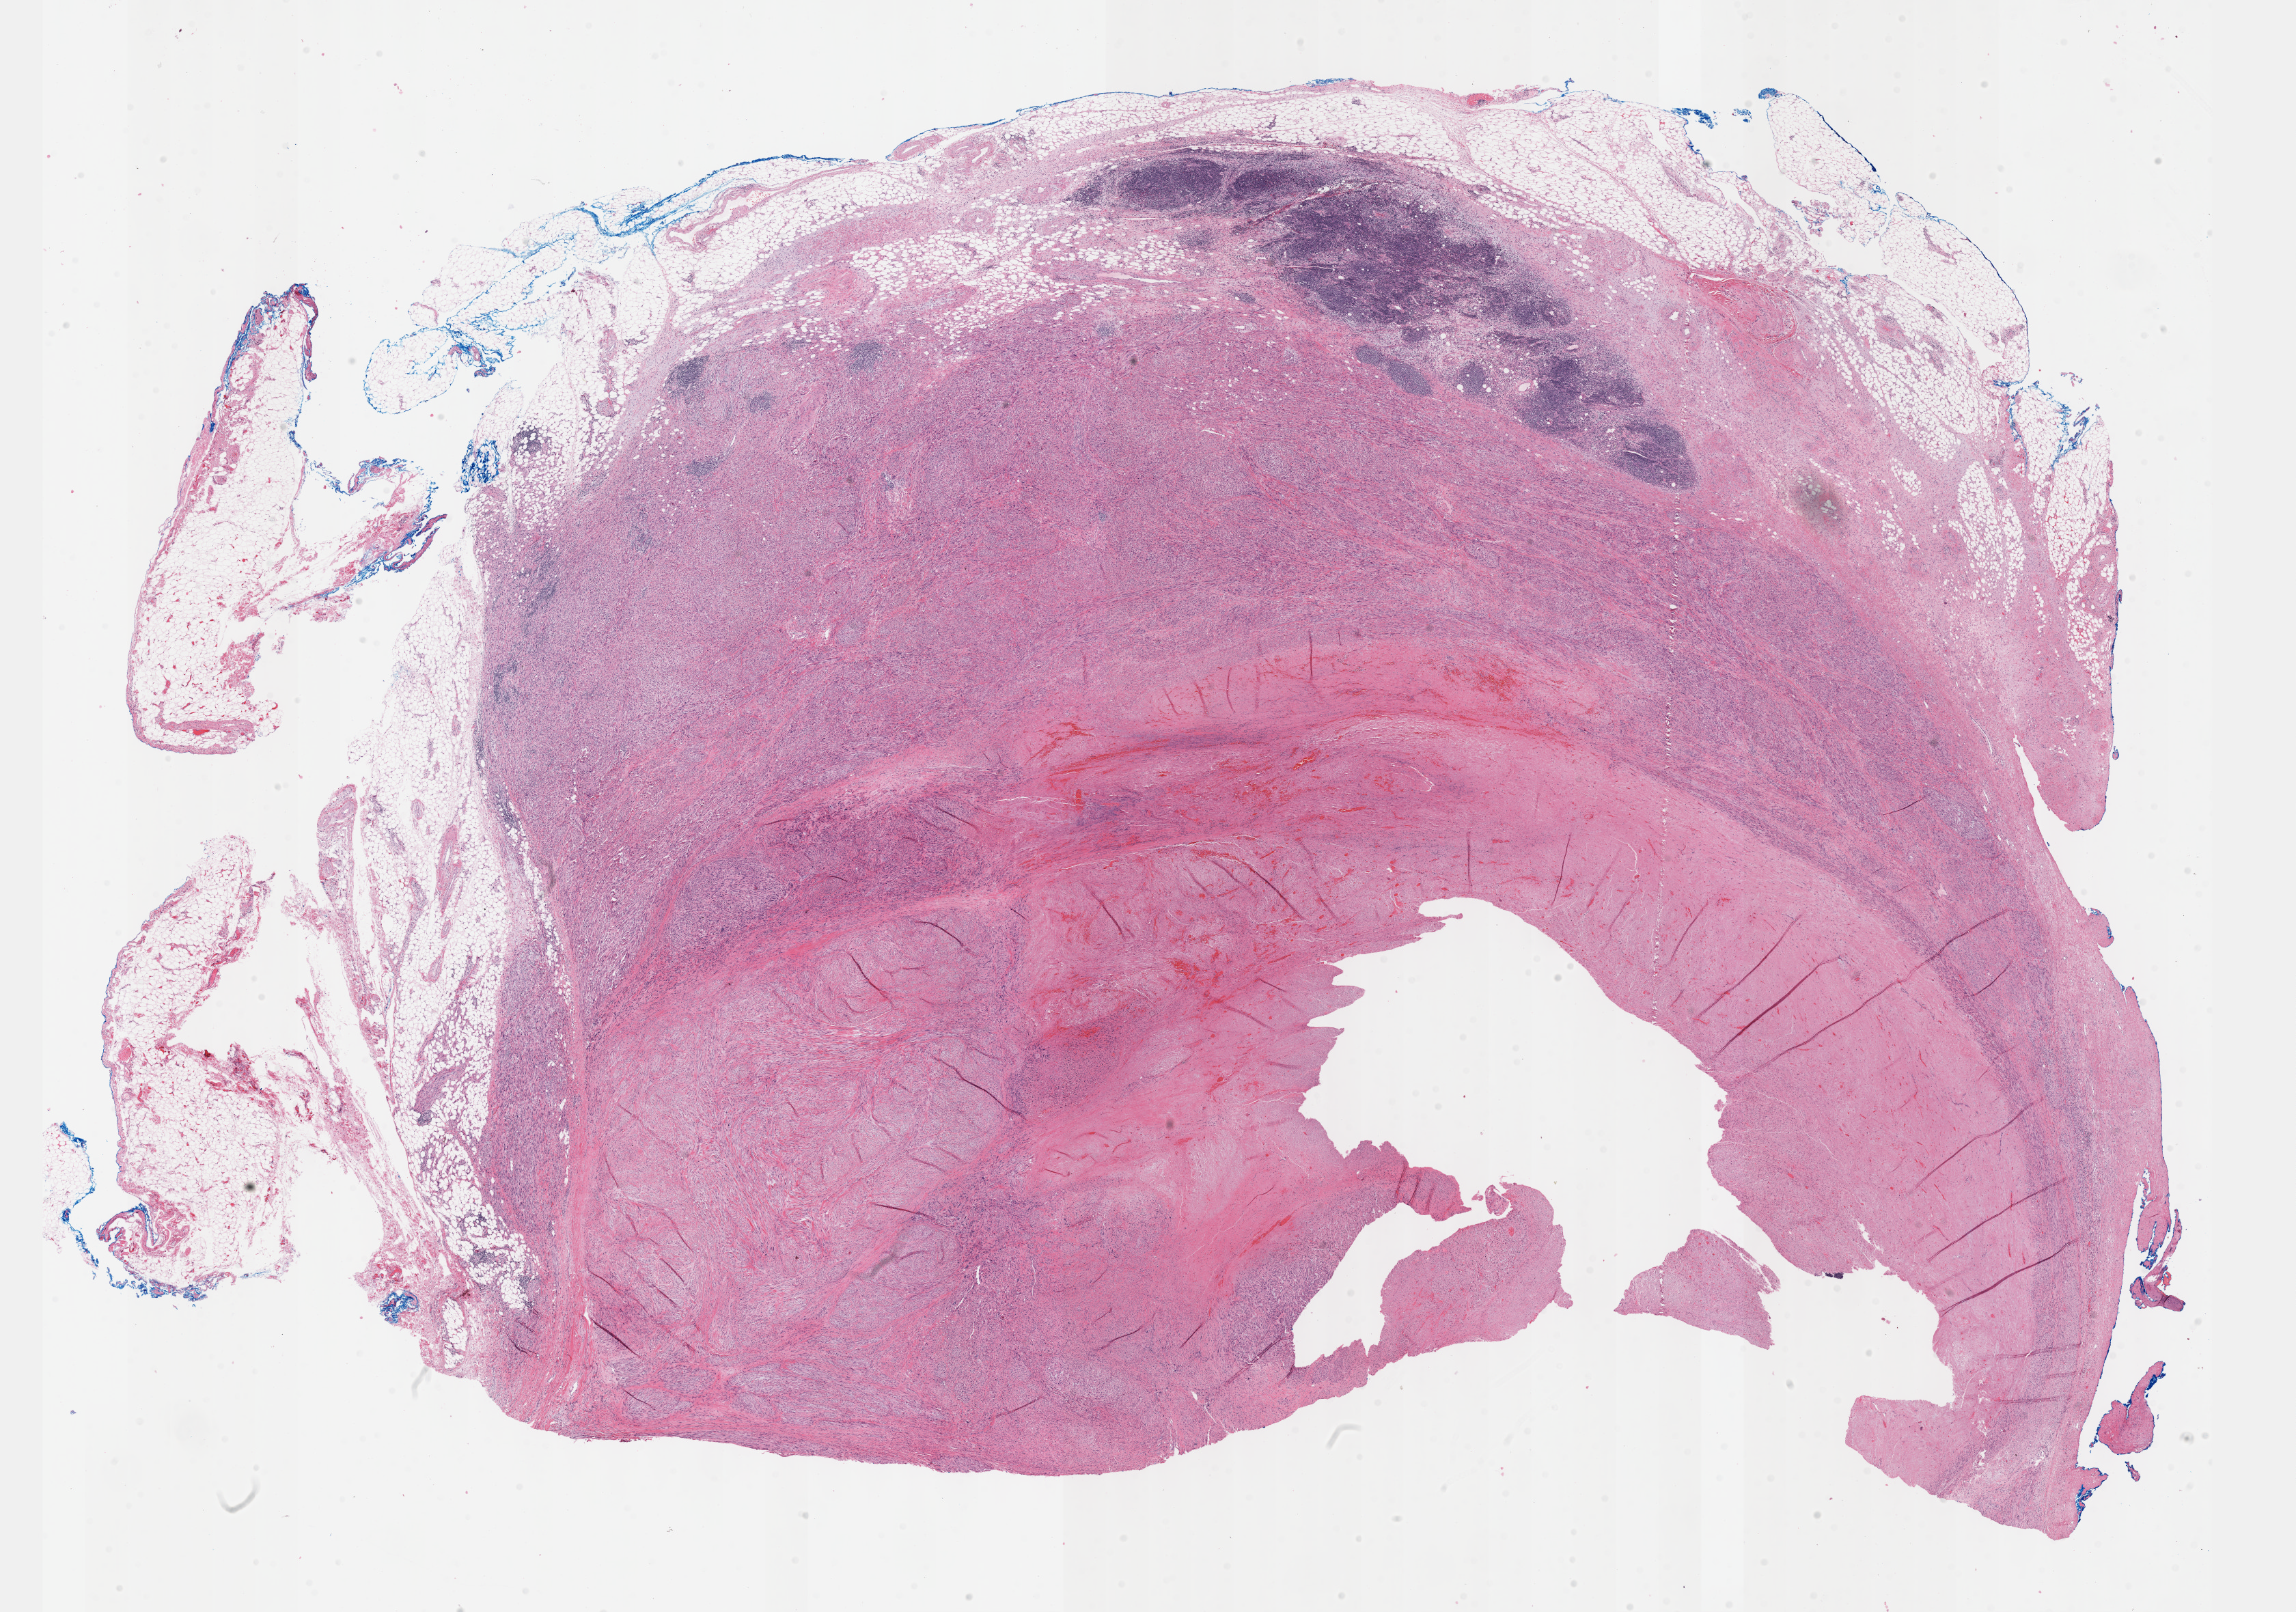
Digitized Hematoxylin and eosin (H&E) stained tissue section (whole slide), a low-resolution overview of the entire scanned area, about 27.2 x 19.1 mm, formalin-fixed paraffin-embedded (FFPE) diagnostic section, sample: primary tumour, connective, subcutaneous and other soft tissues. Female patient.
- diagnosis: Leiomyosarcoma, NOS (connective, subcutaneous and other soft tissues of thorax)